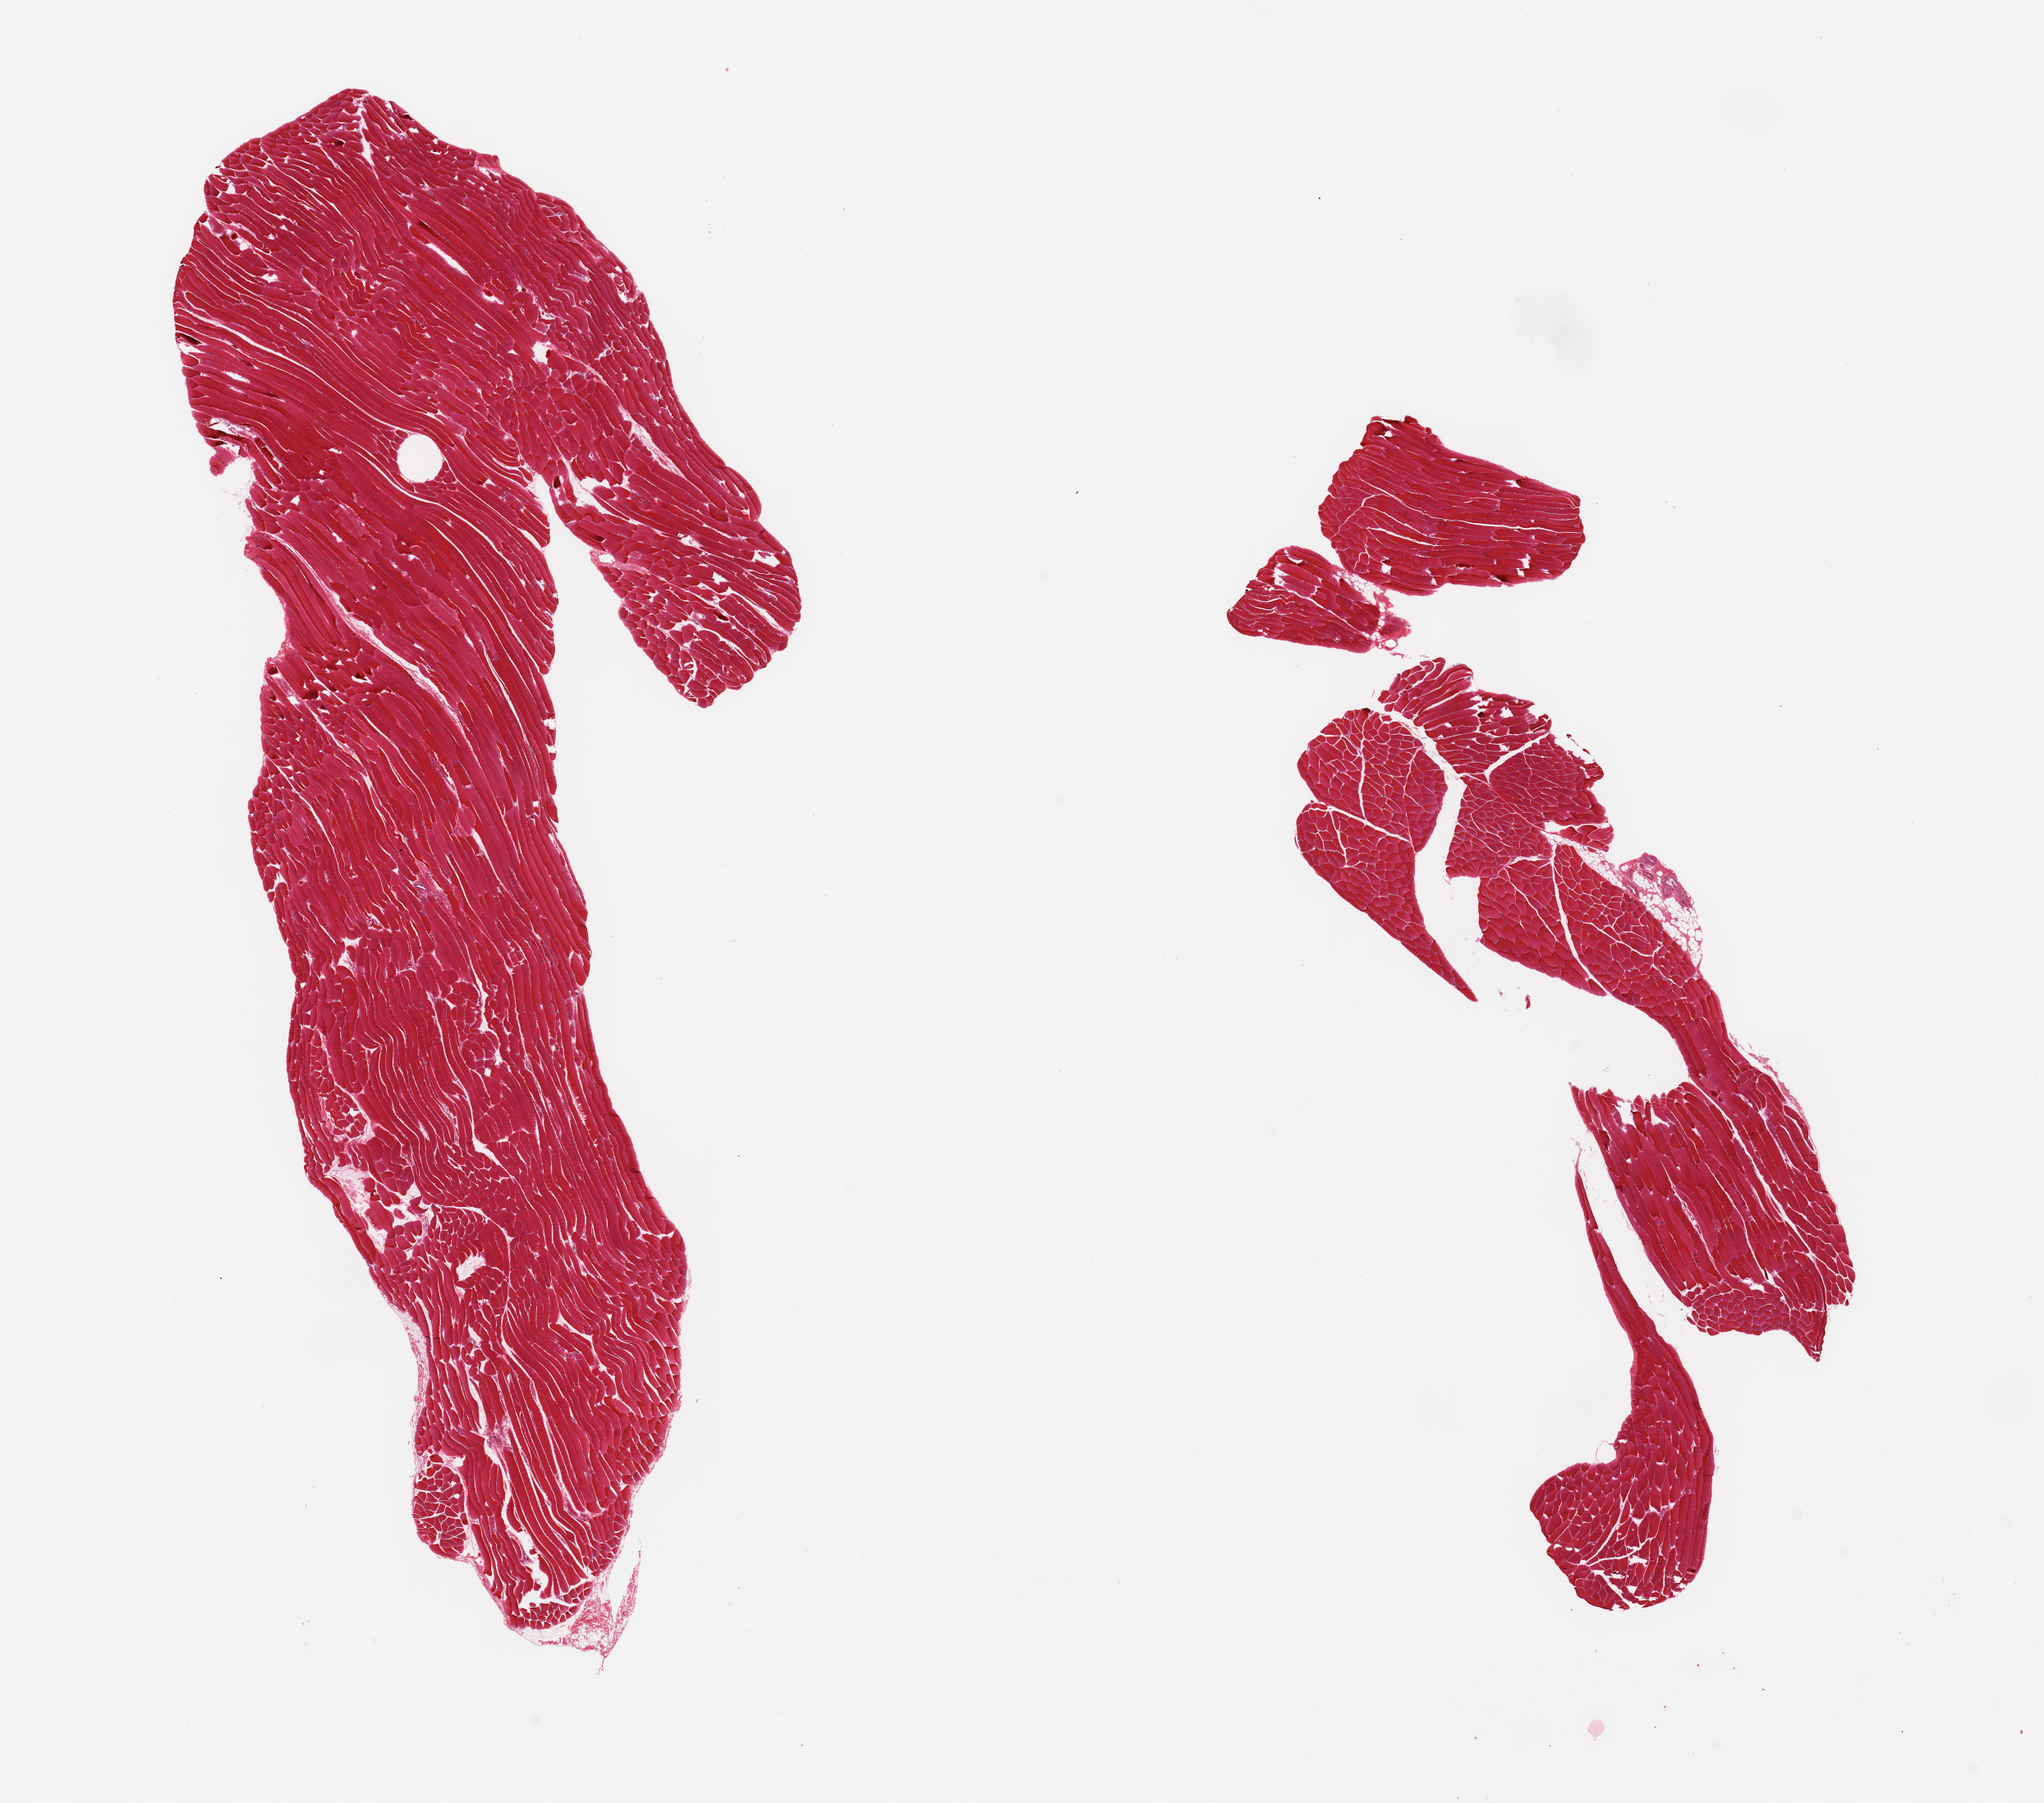
Whole-slide image, haematoxylin and eosin stain — whole scanned area (about 19.7 x 17.4 mm, from a 20x scan) shown as a low-resolution overview. PAXgene-fixed, paraffin-embedded tissue. Section of skeletal muscle (target tissue). Tissue donor sample. Male donor.
• review note (as recorded): 2 pieces